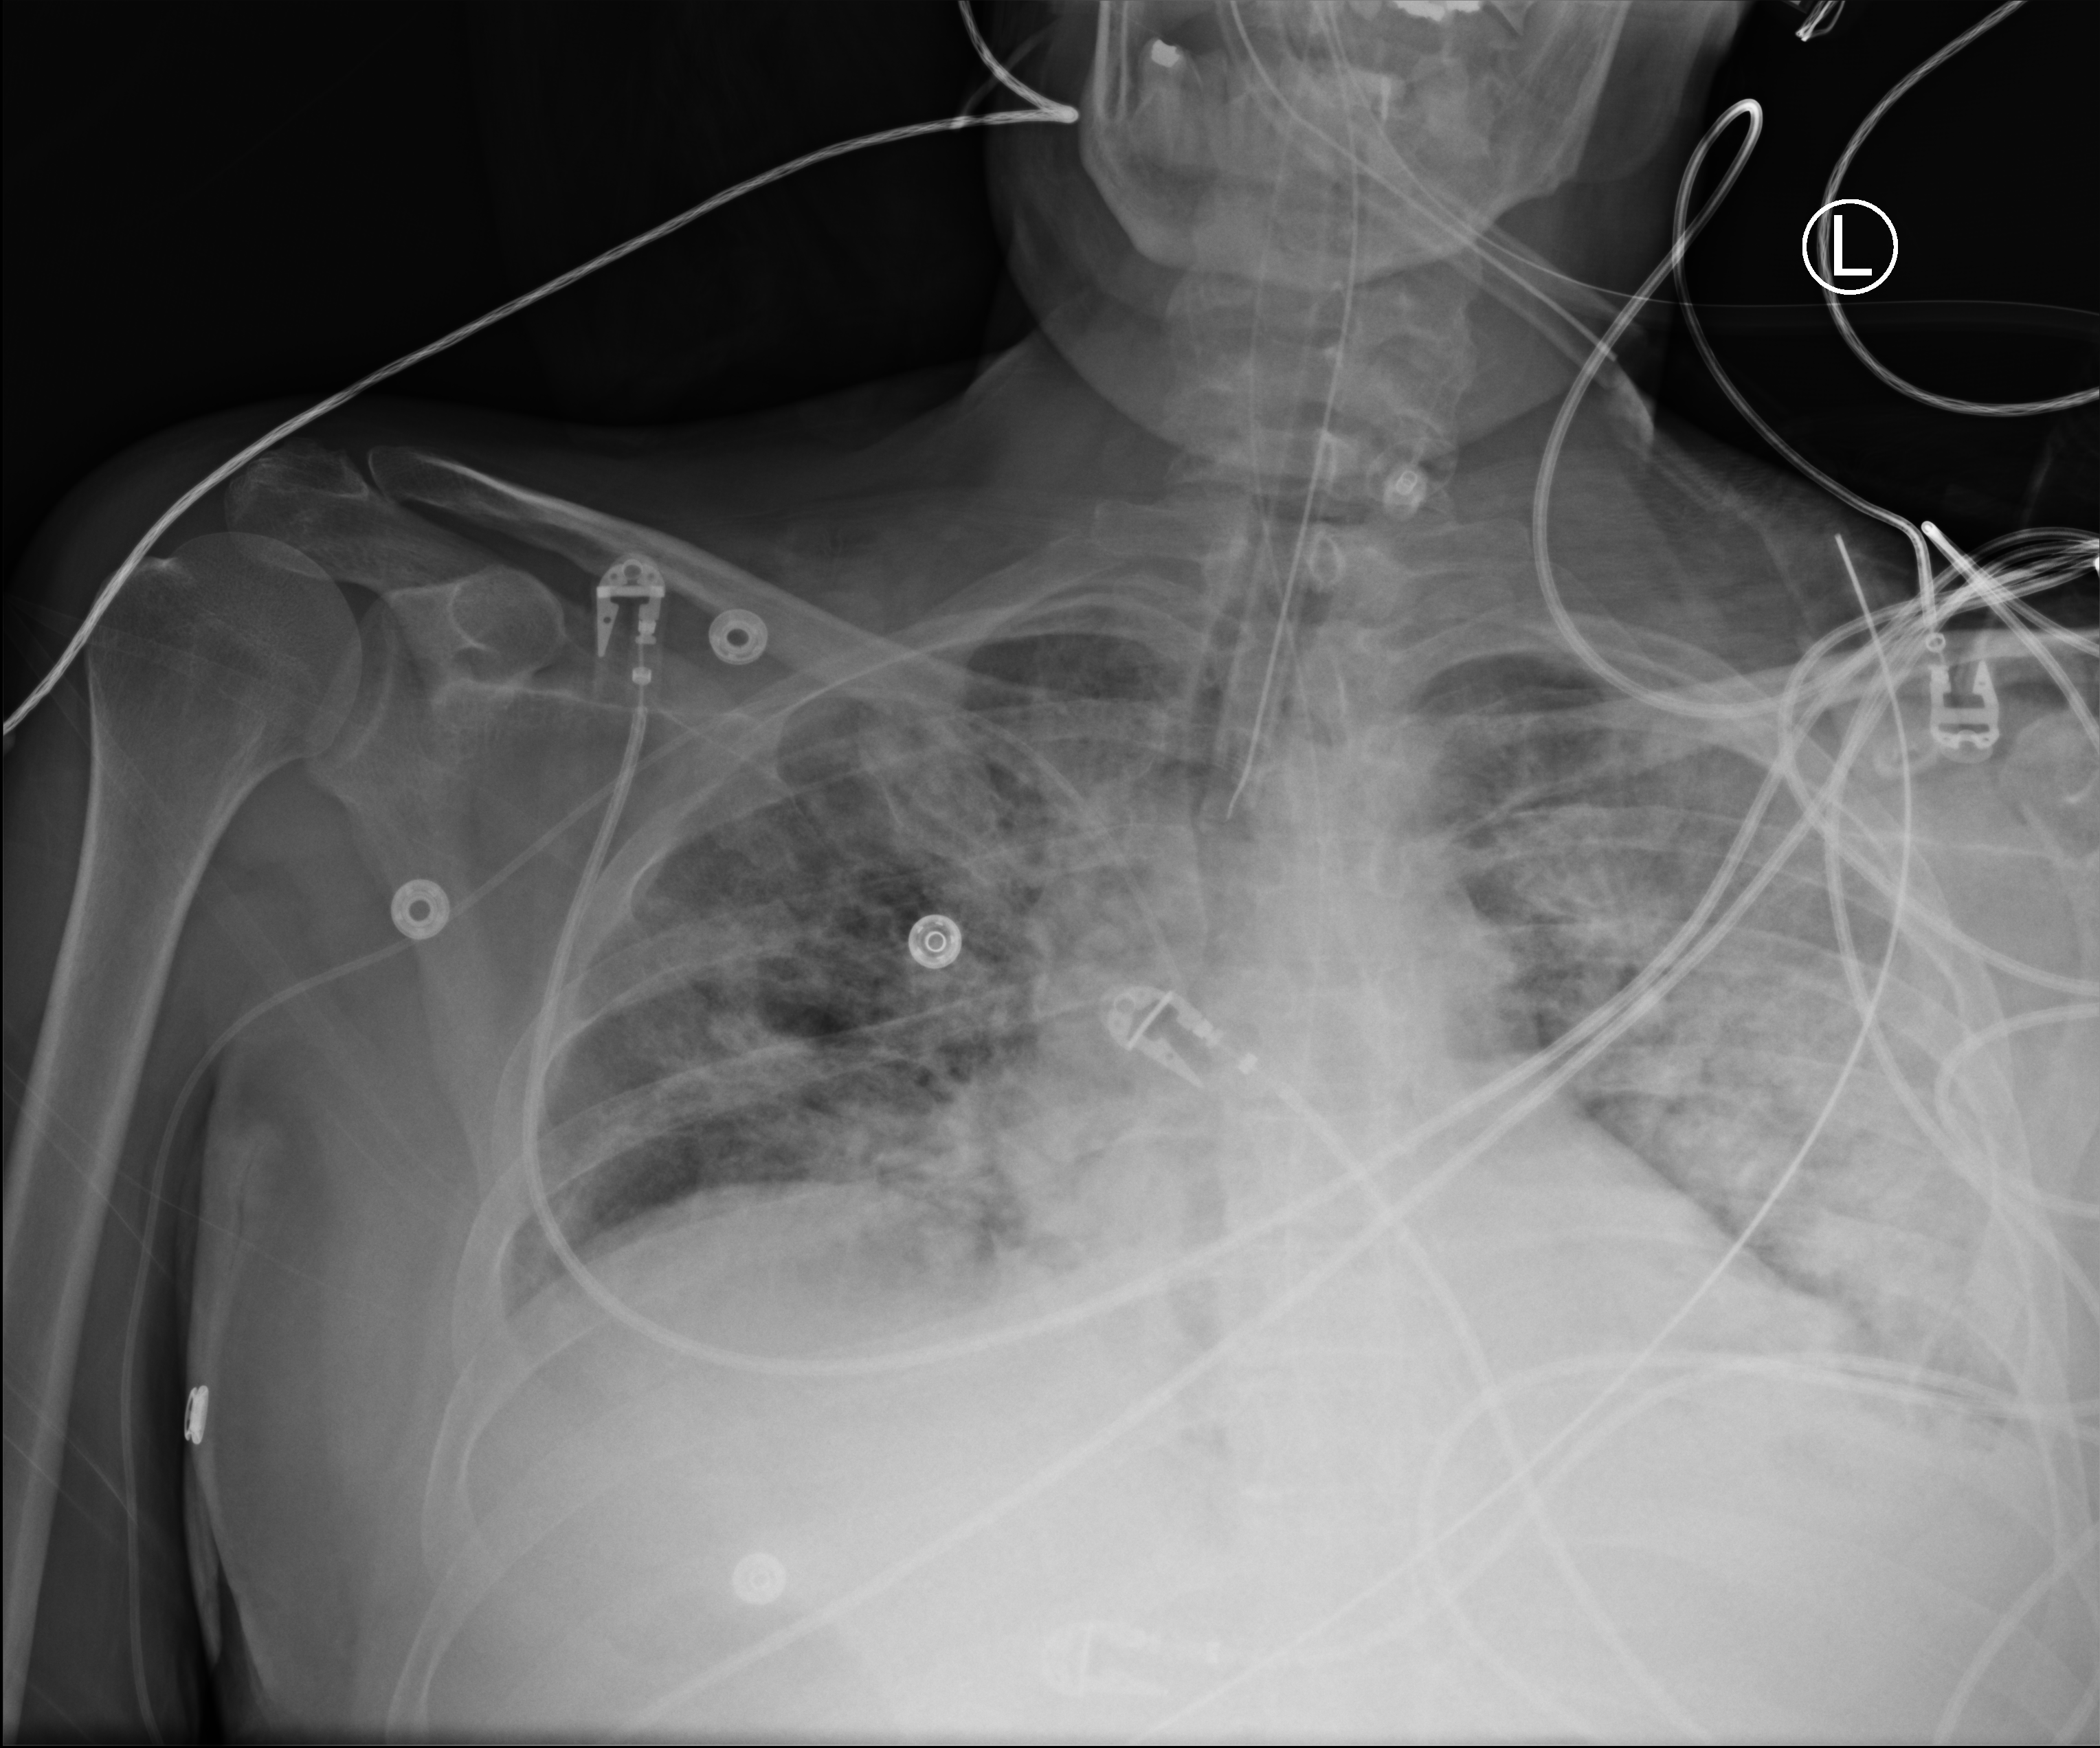
Chest X-ray (portable), anteroposterior (AP) projection. Male patient hospitalised with COVID-19, age 18–59 years.
Admission-level facts for this patient (not findings on this image; timing relative to this image not recorded): admitted to intensive care during this hospital stay: yes; length of hospital stay: 48 days.